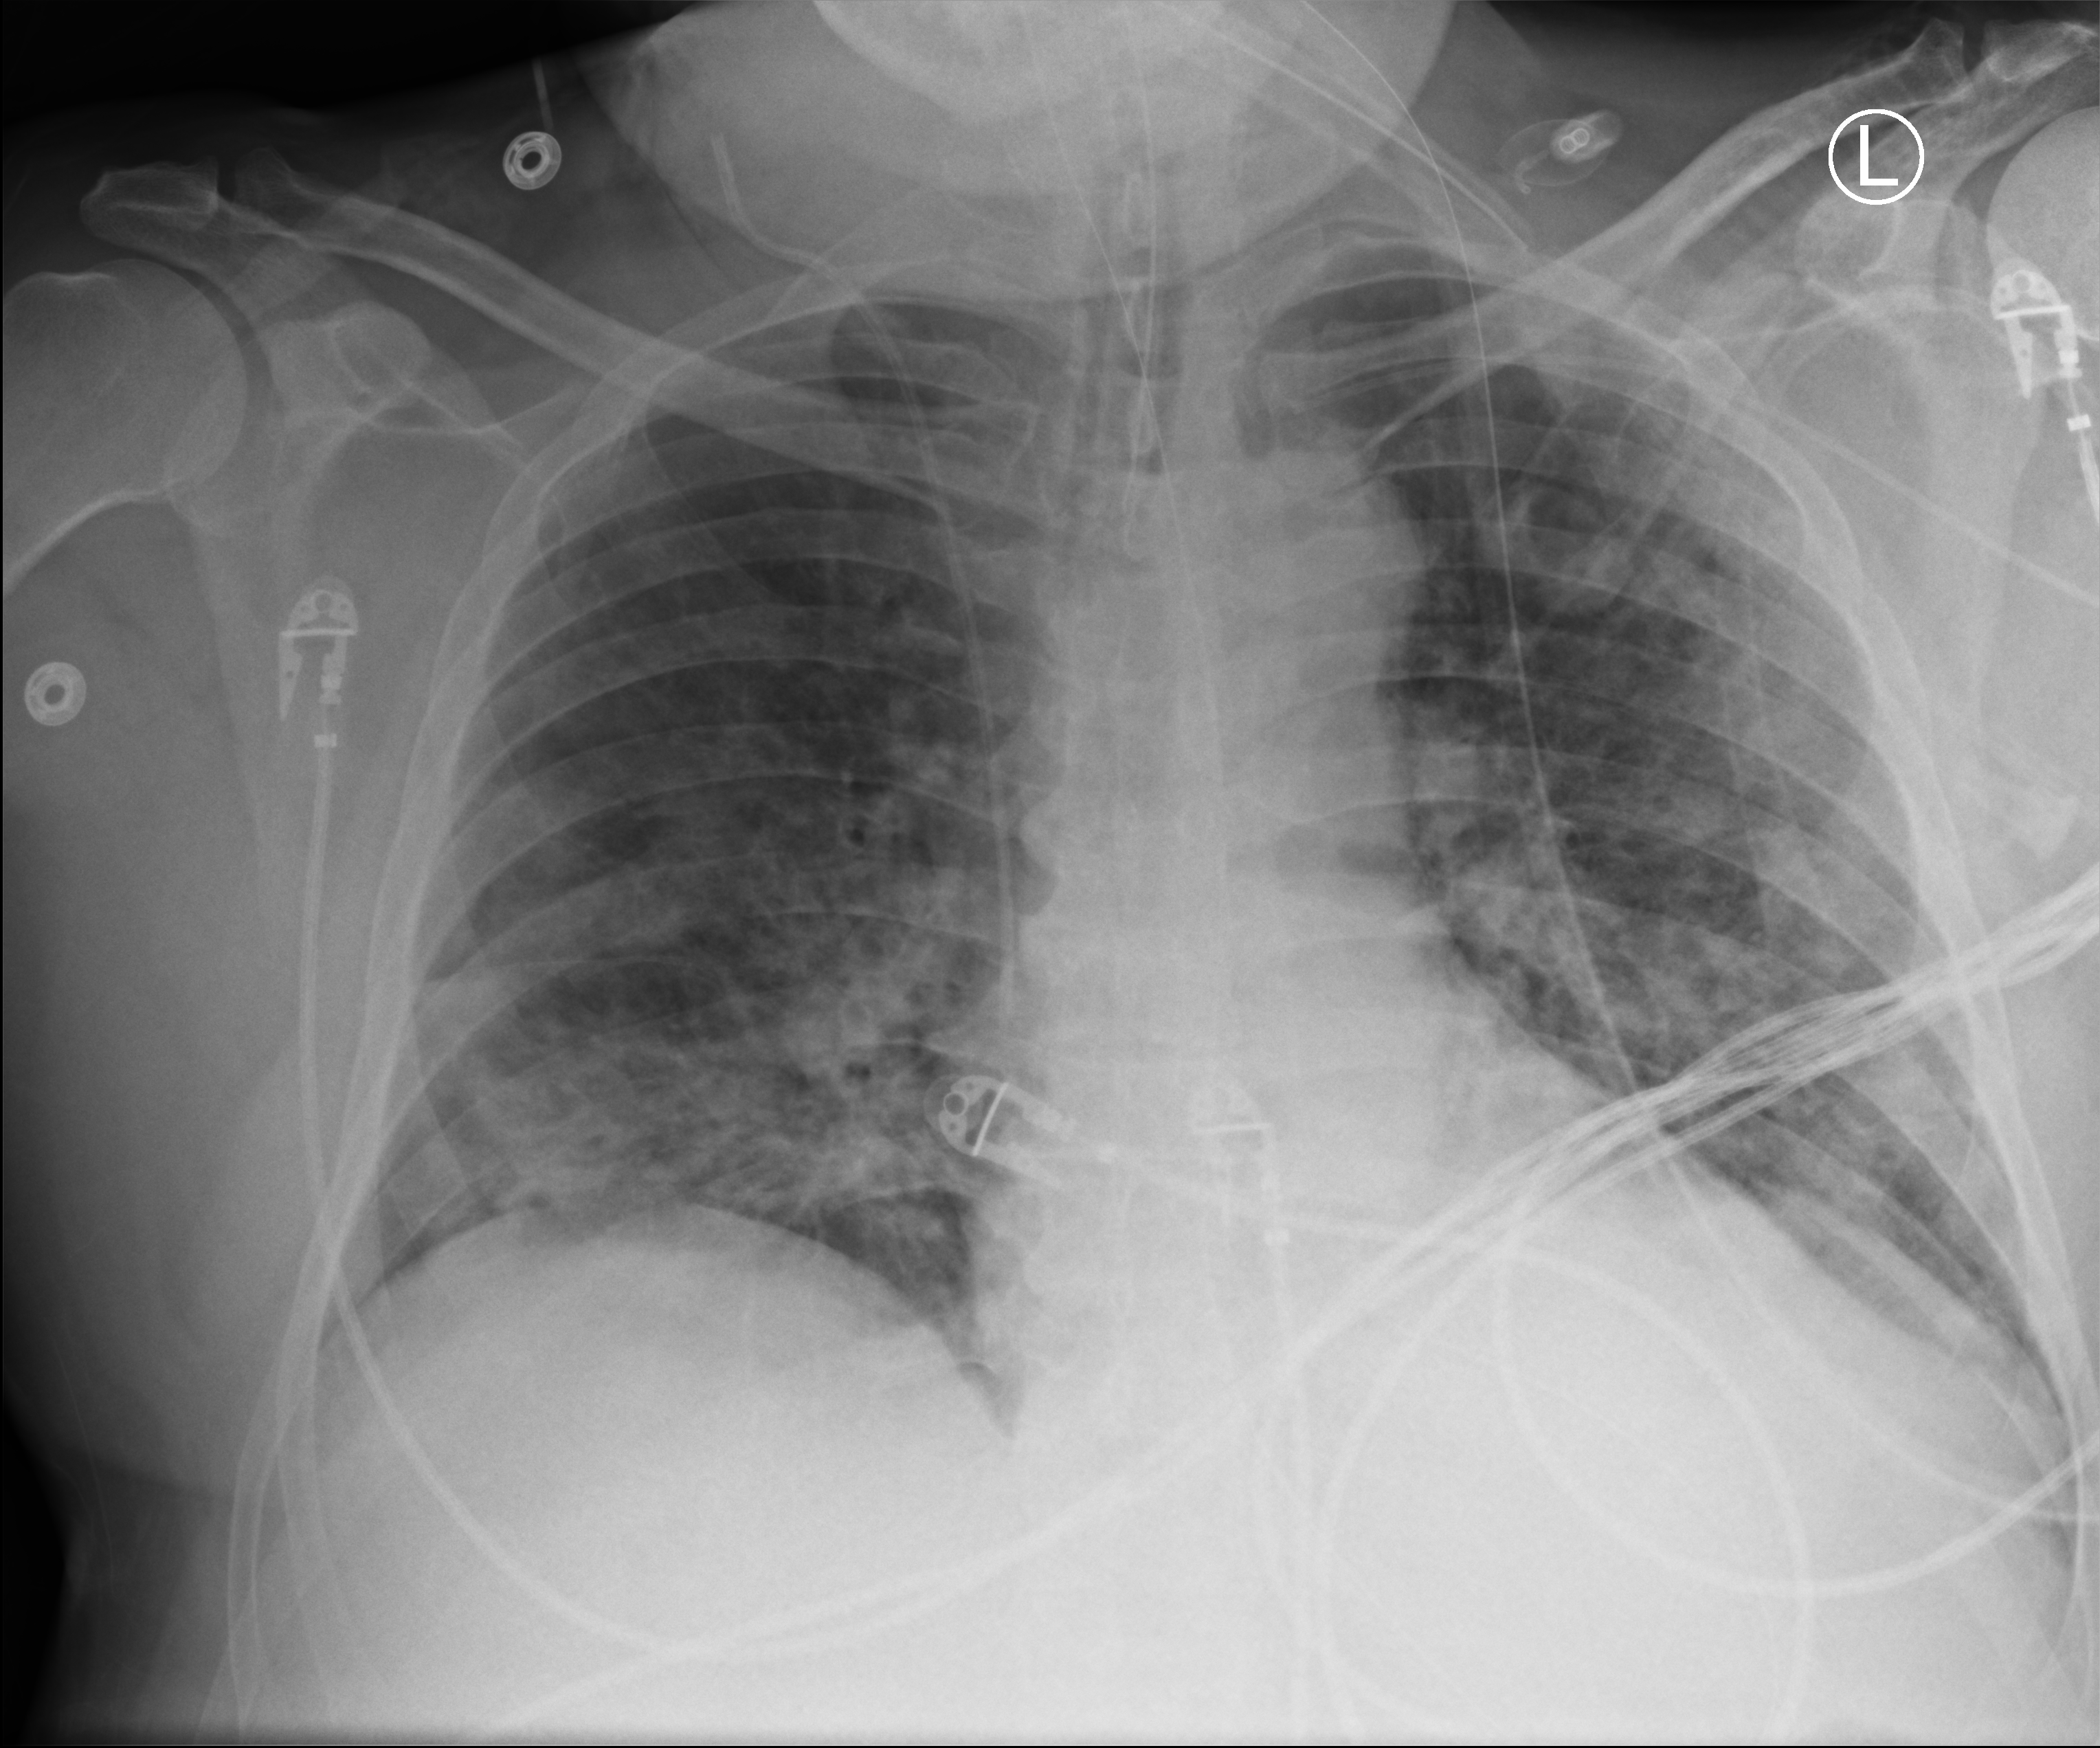
Portable chest radiograph, anteroposterior (AP) projection. Patient hospitalised with COVID-19; male, aged 60–74 years.
Hospital-stay facts (about this admission, not read from this image; timing relative to this image not recorded):
- mechanically ventilated during this hospital stay: yes
- admitted to intensive care during this hospital stay: yes